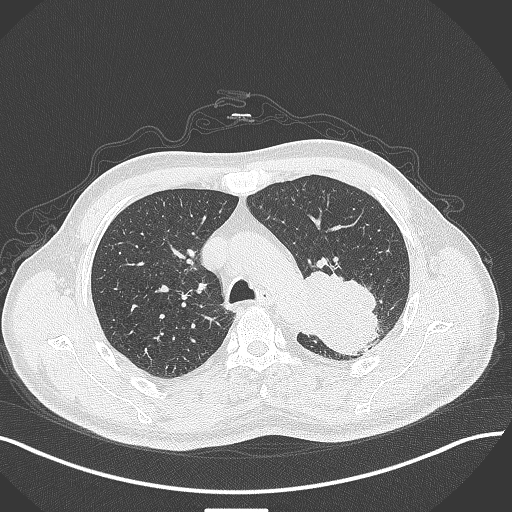
Chest CT, one axial slice. Slice 307 of 429 in the series (ordered by position). 120 kVp. Lung window (W 1500 / L -600 HU). 512 × 512 image matrix, field of view 400 × 400 mm. Male patient, age 55 years. Case-level facts recorded for this patient, not image findings: clinical TNM (as recorded): T3 N0 M1c.
Outlined on this slice (bounding box drawn by a radiologist):
- lung tumour (recorded histology: adenocarcinoma): bounding box <293,266,387,361> (left, top, right, bottom; pixels)